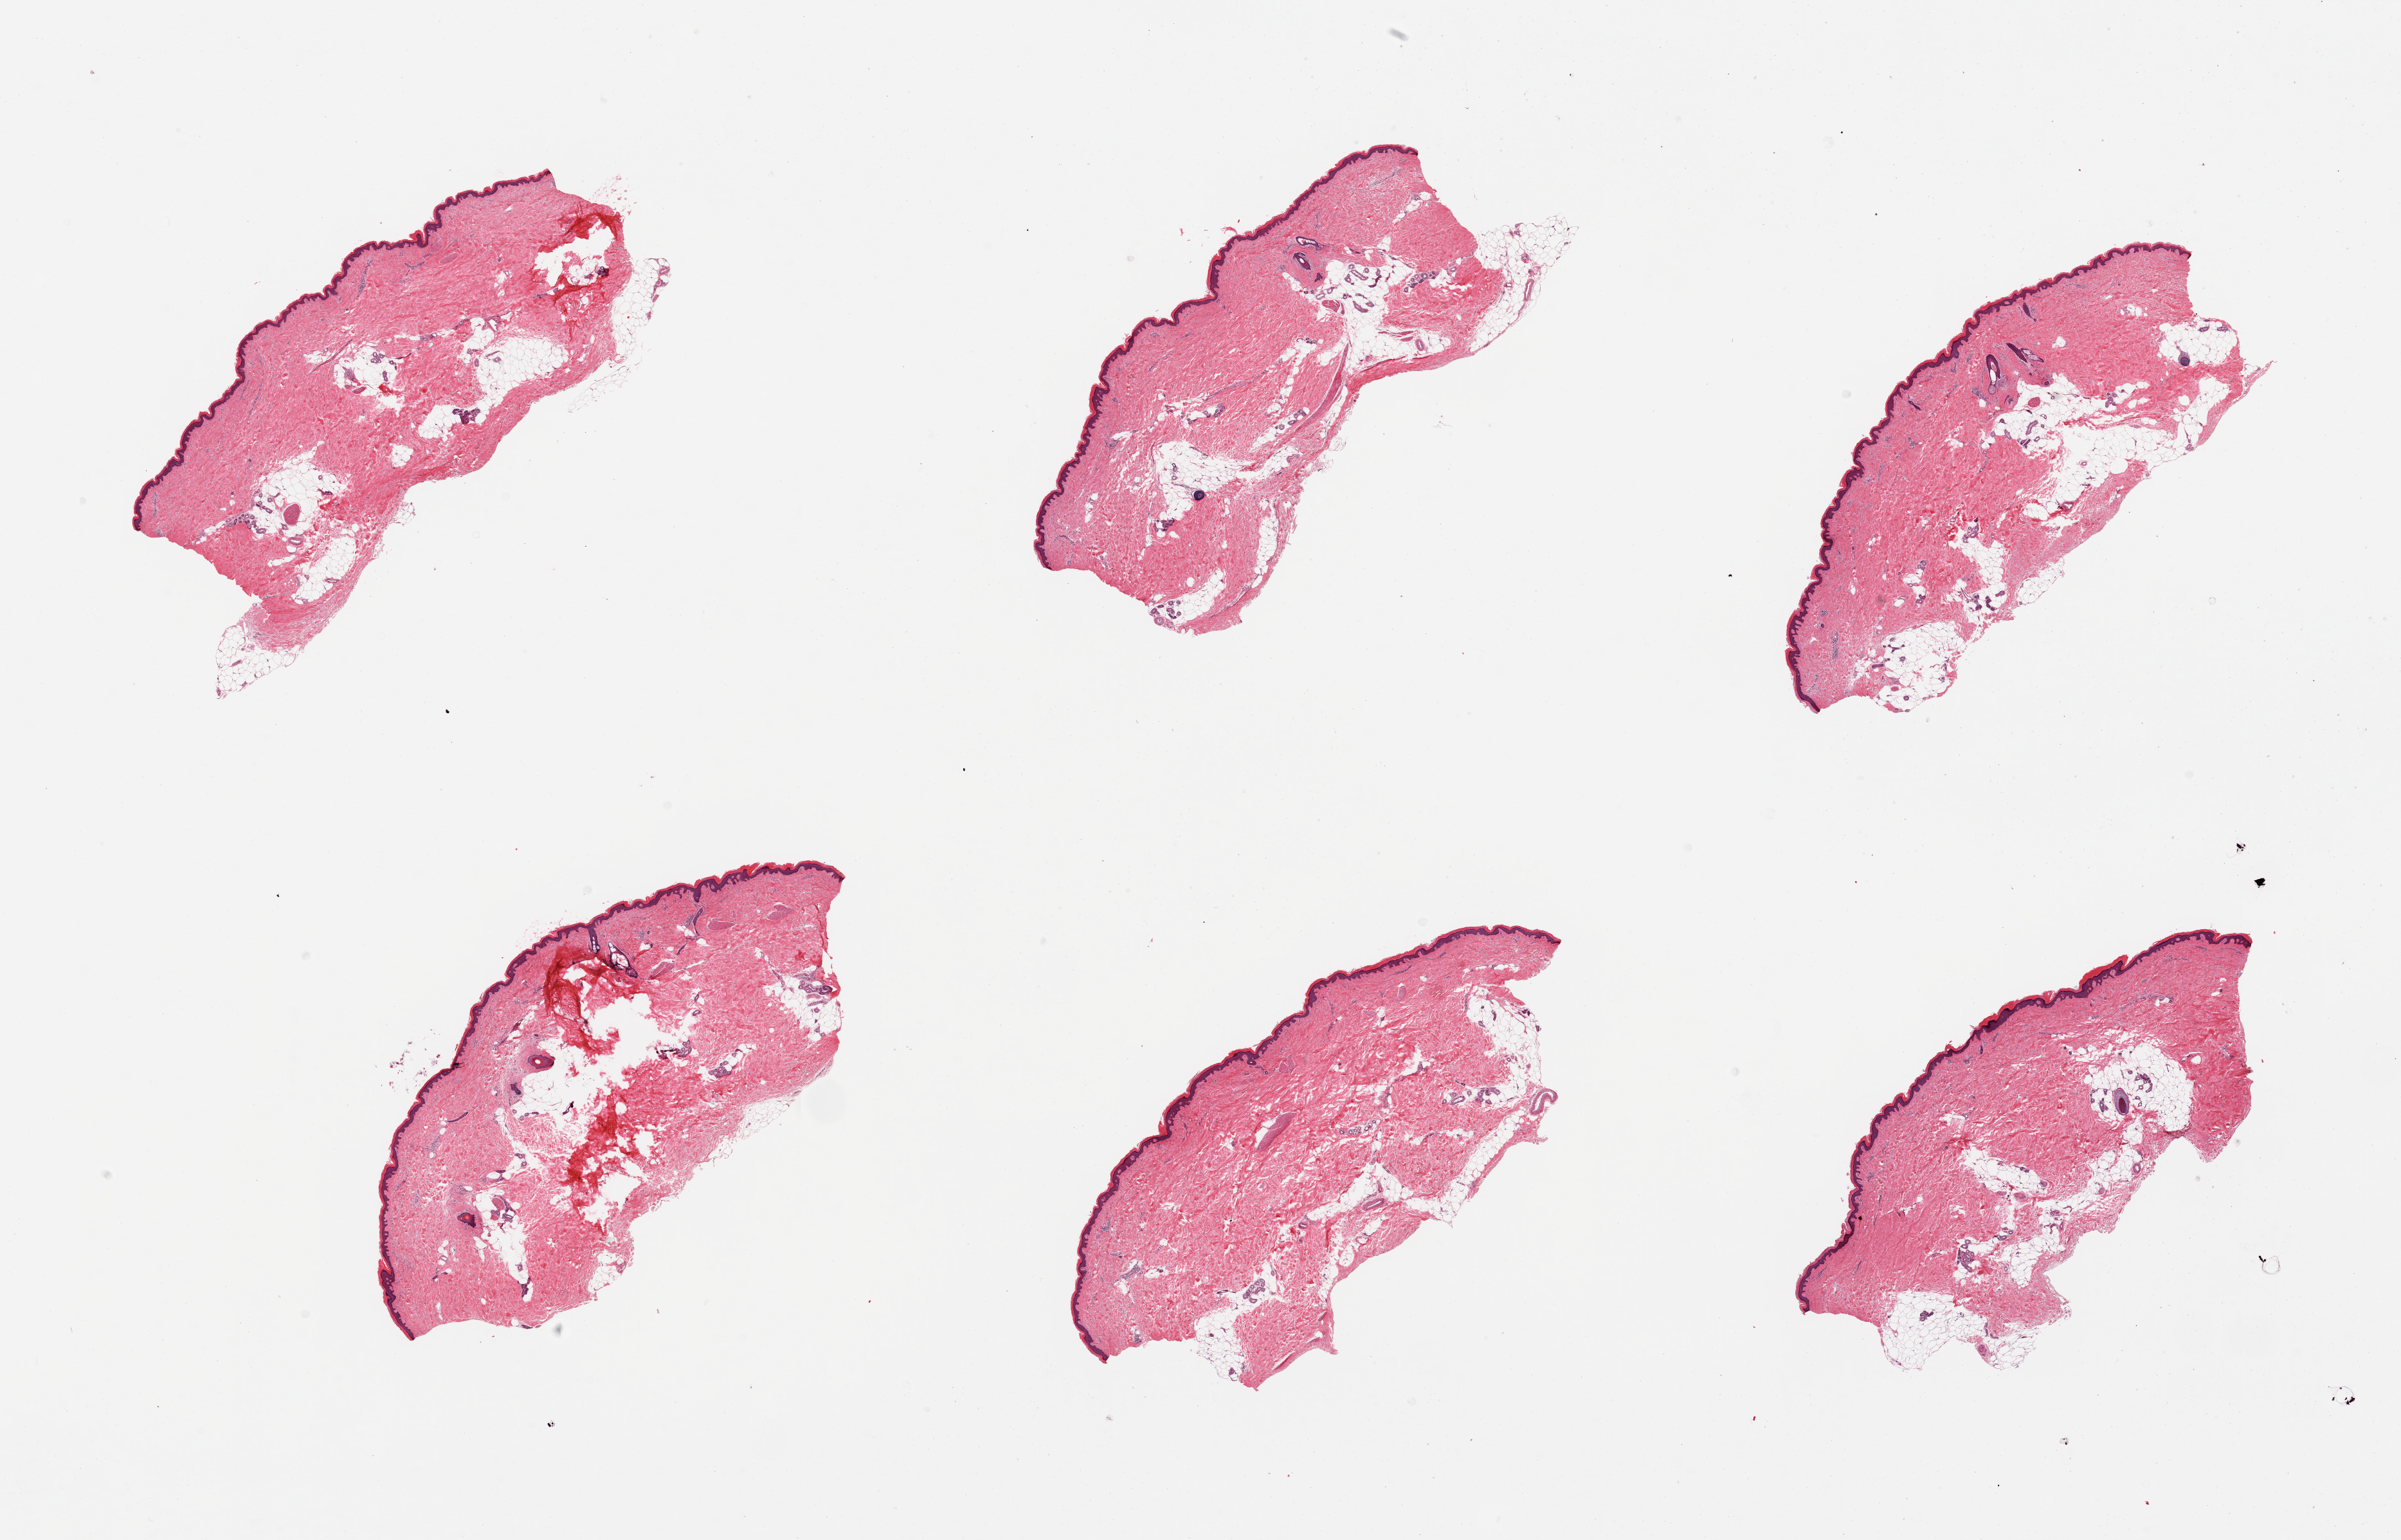
Digitized hematoxylin and eosin (H&E)-stained section — a low-resolution overview of the entire scanned area, about 29.5 x 18.9 mm; PAXgene-fixed, paraffin-embedded tissue; target tissue: skin of lower leg; donor tissue sample. Female donor.
Reviewer comment on this tissue sample: 6 pieces, minimal adherent dermal fat. Squamous epithelium is ~7-90 microns thick.